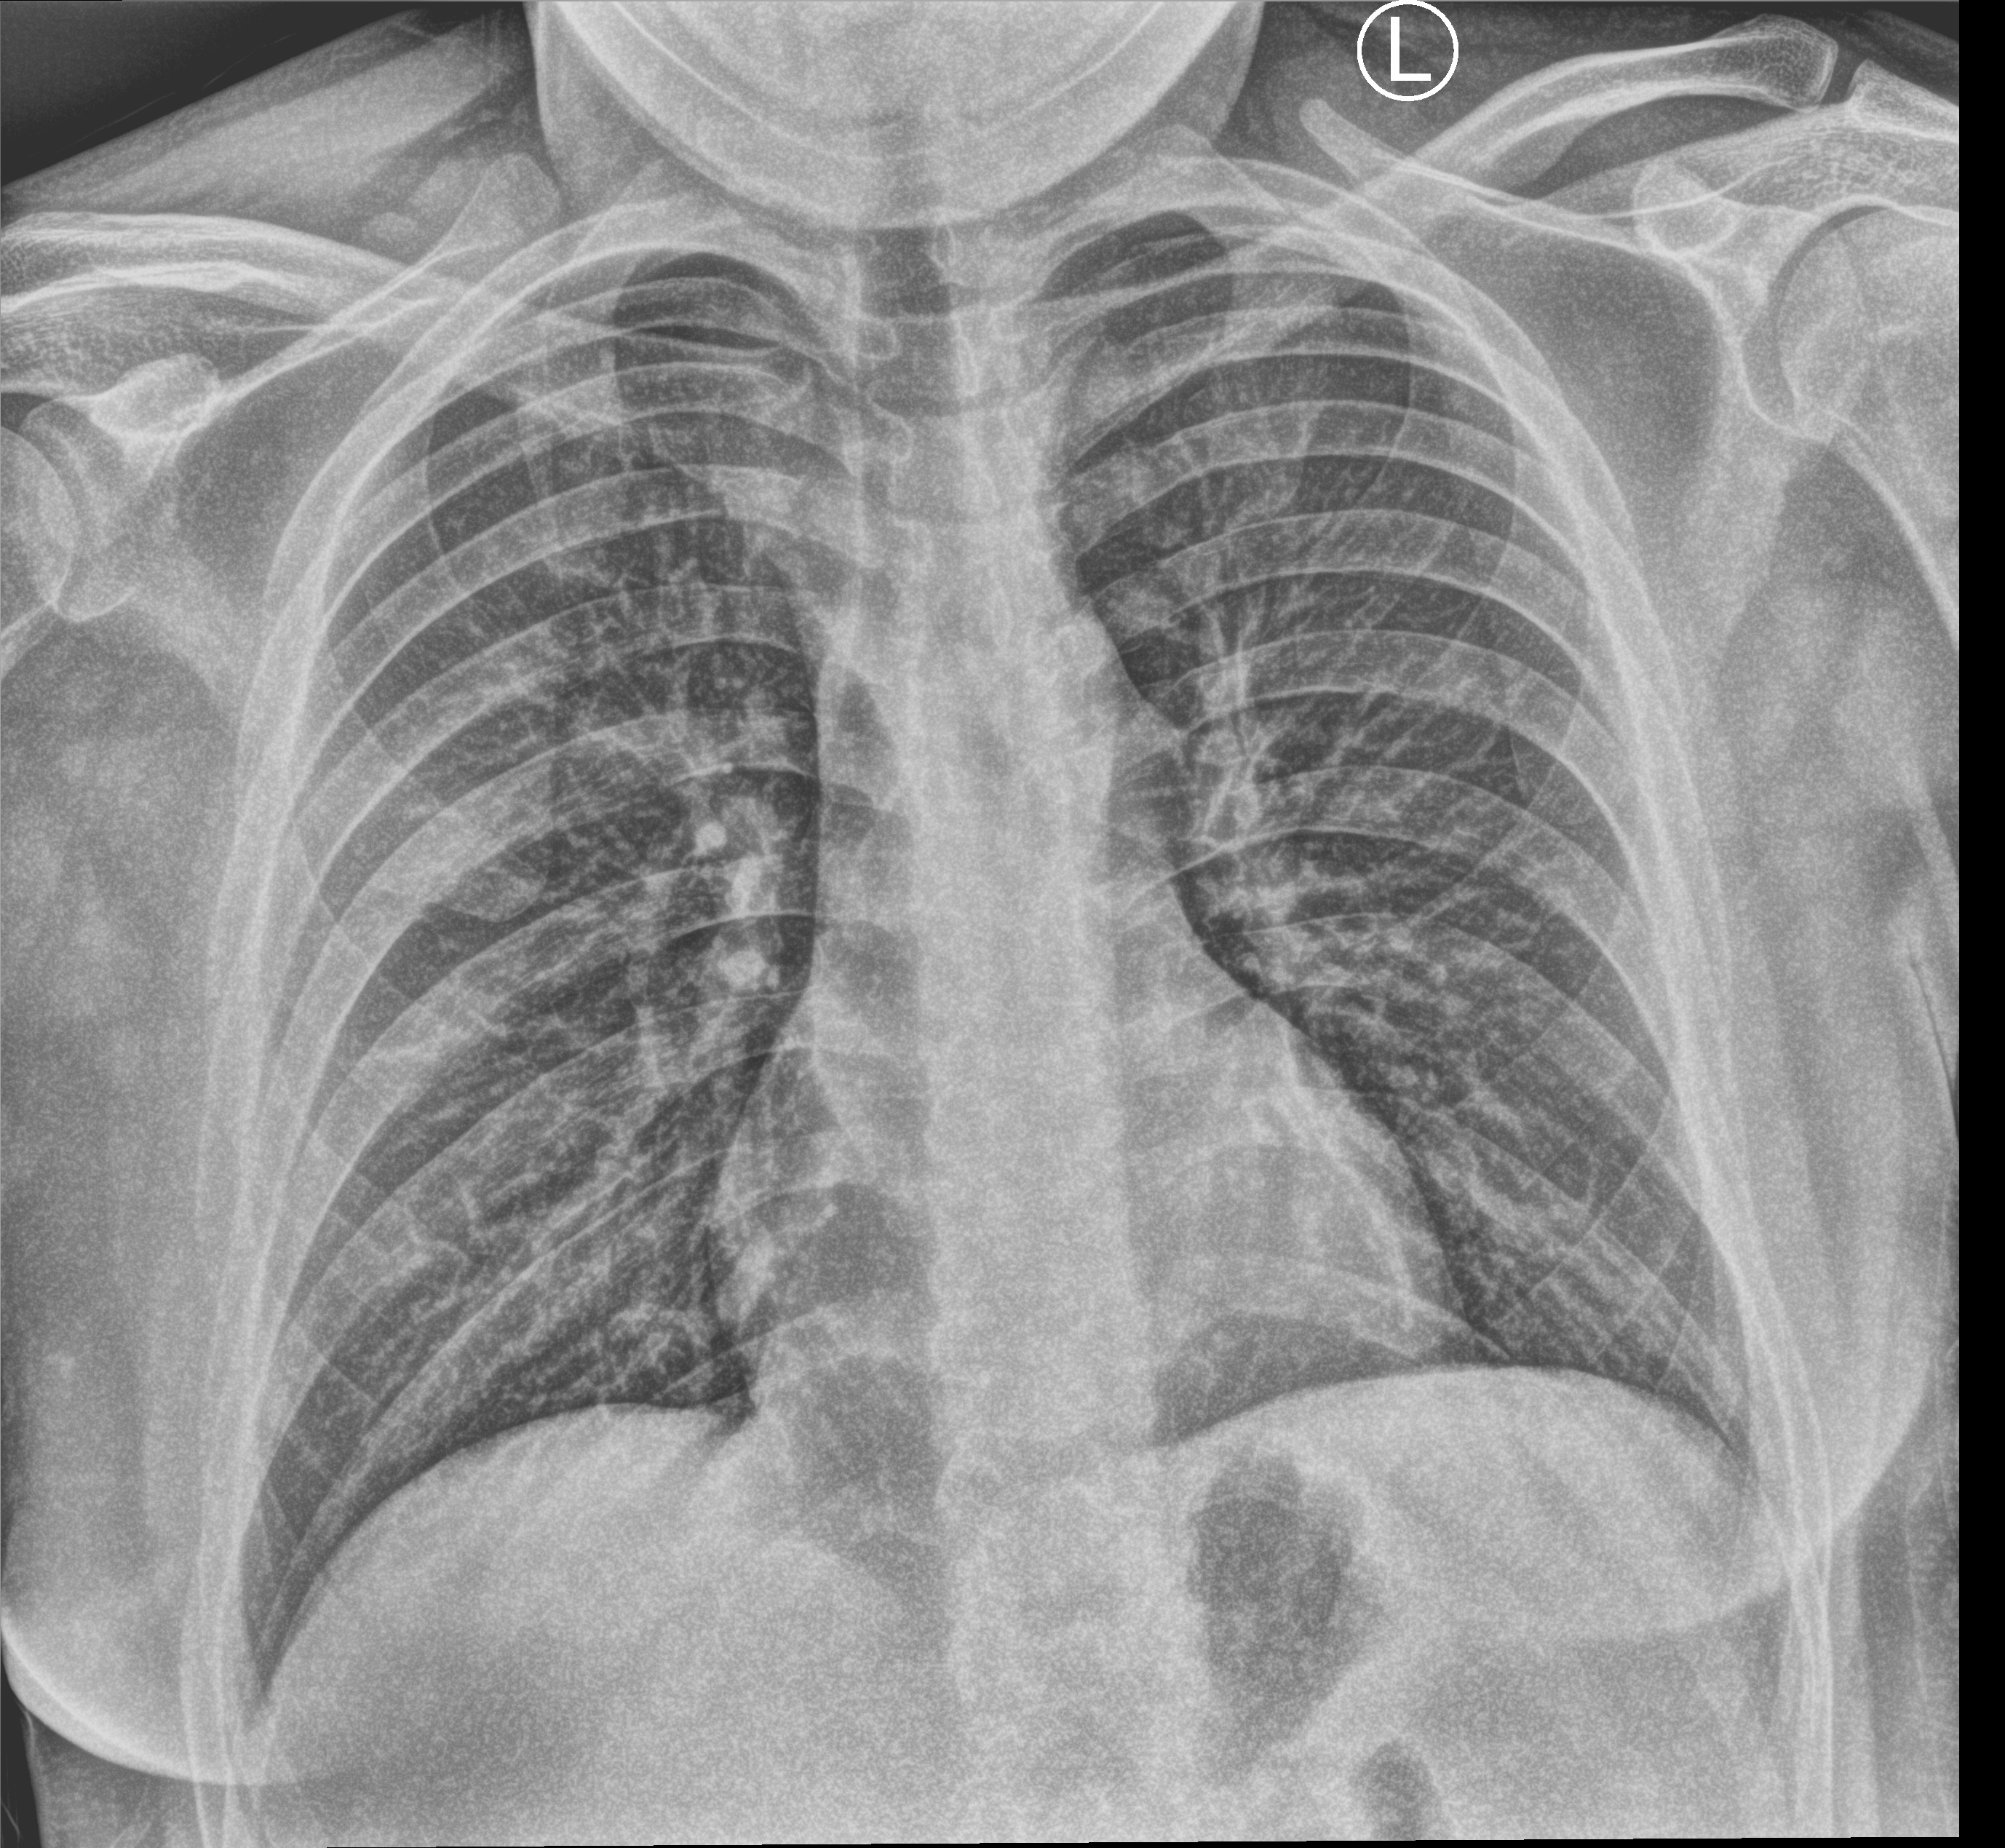
Portable chest radiograph; anteroposterior (AP) projection. Male patient hospitalised with COVID-19, age 18–59 years.
From the hospital-stay record, not from the radiograph (when in the stay this image was taken is not recorded): length of hospital stay: 7 days; mechanically ventilated during this hospital stay: no.